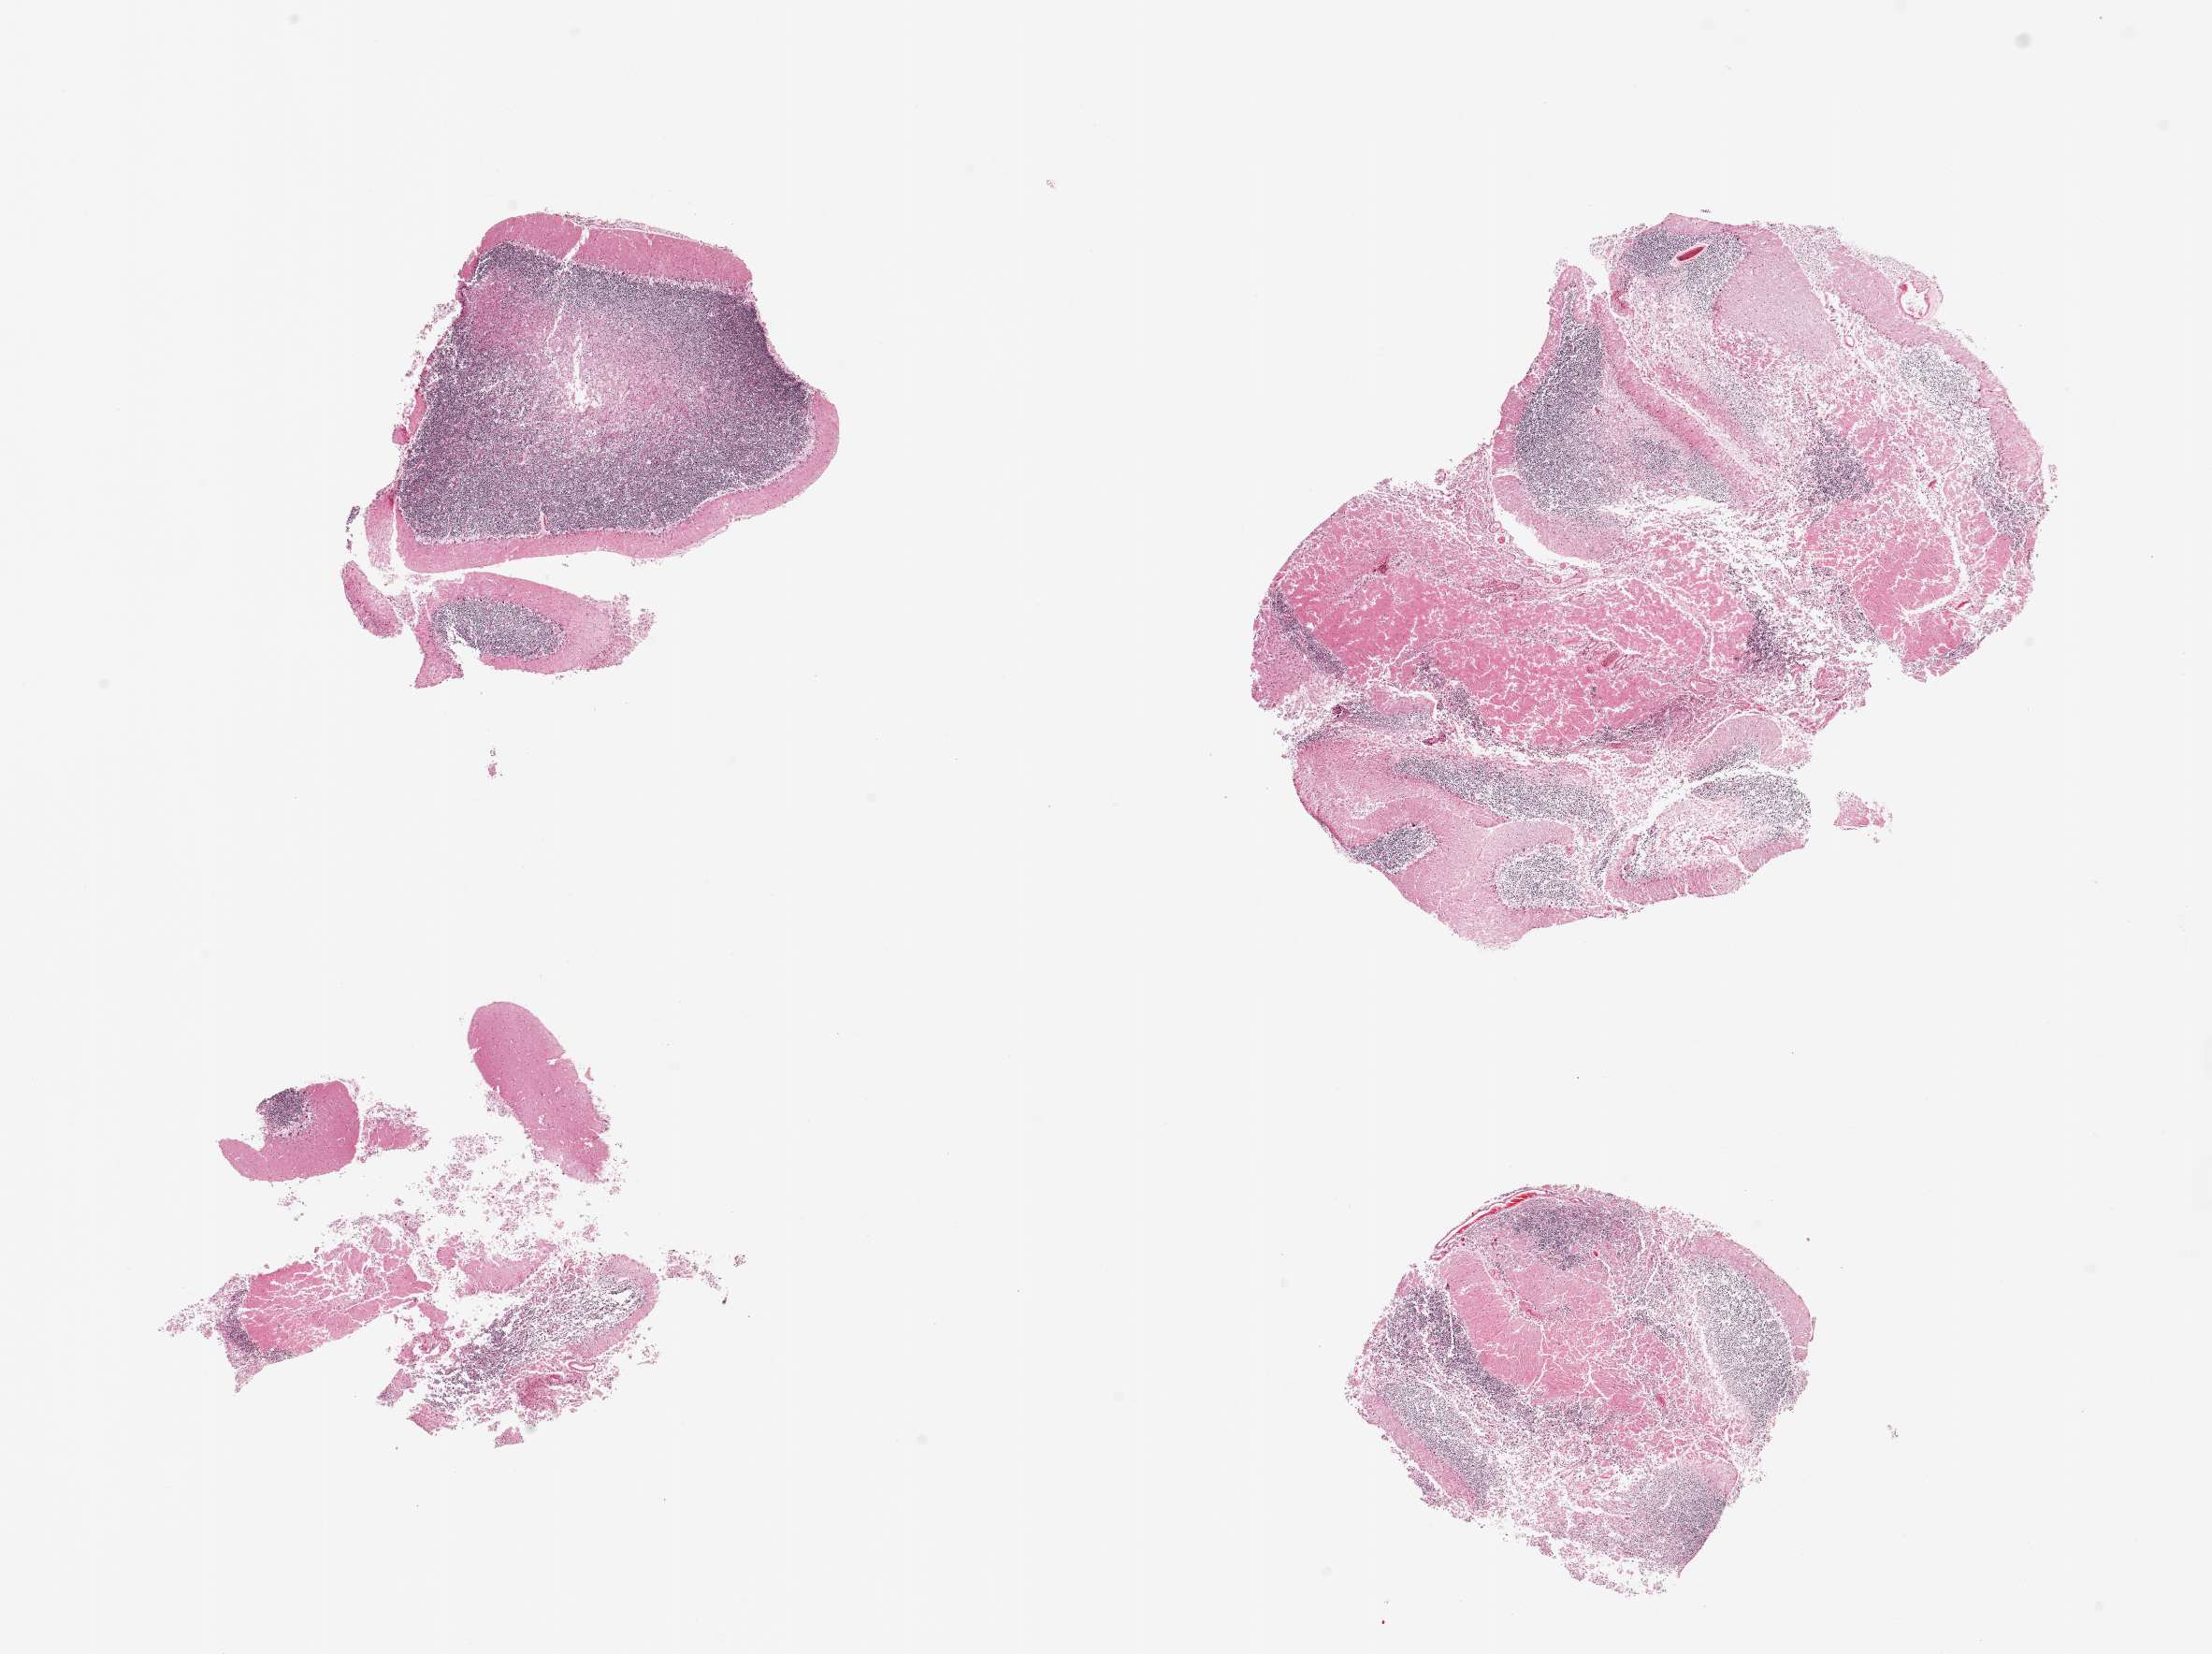
Whole-slide image, haematoxylin and eosin stain — shown as a low-resolution overview of the whole scanned area (about 18.7 x 14.0 mm, slide scanned at 20x); PAXgene-fixed, paraffin-embedded tissue; sampled site (target tissue): cerebellum; tissue donor sample.
- reviewer comment on this tissue sample: 4 pieces; fragmented and predominantly autolyzed